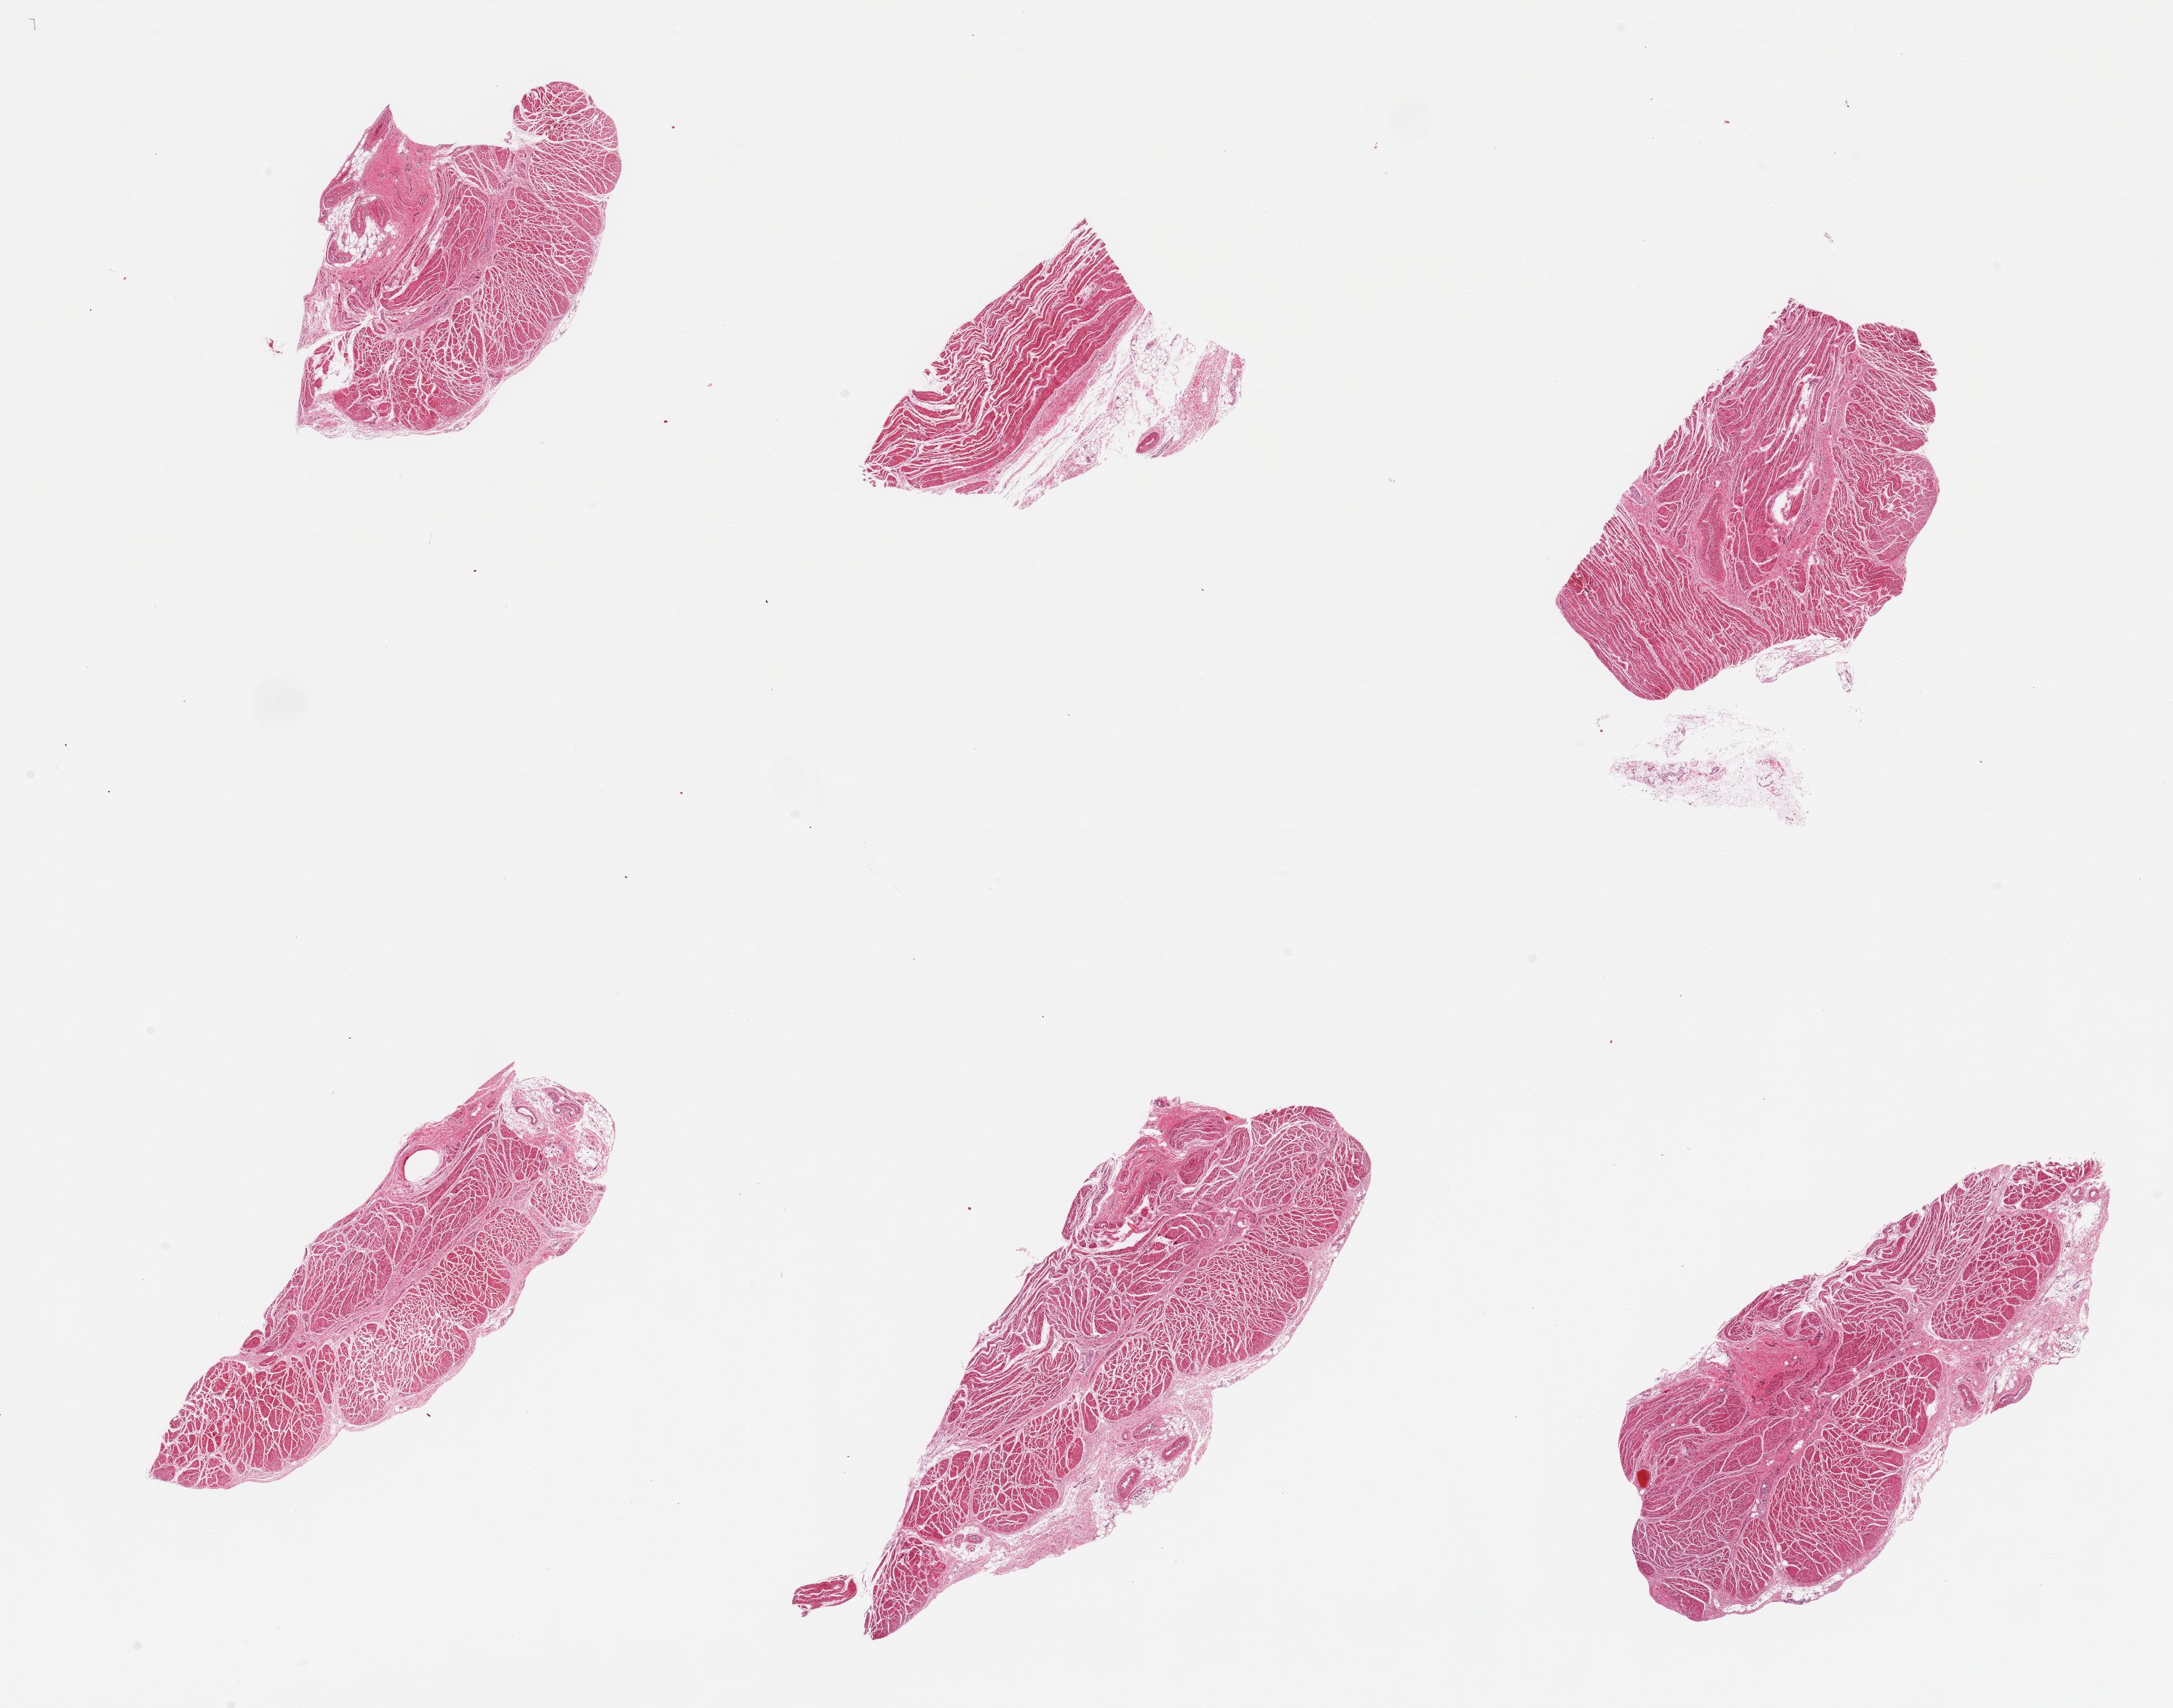
Whole-slide image, H&E stain, low-resolution overview of the scanned area, about 23.6 x 18.6 mm (slide scanned at 20x). PAXgene-fixed, paraffin-embedded tissue. Section of gastroesophageal junction (target tissue). Donor tissue sample. Donor sex: male.
Pathologist's review note for this sample: 6 pieces, confirmed target muscularis.